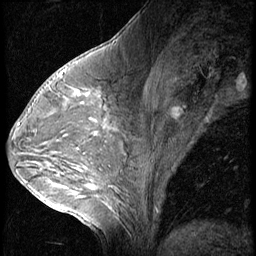
Breast MRI (dynamic contrast-enhanced), one sagittal slice. Position 31 of 56 along the scan axis. 3 images stored at this slice position (order not interpretable as contrast timing). 1.5 T. TE 4.2 ms, TR 9 ms. 256 × 256 image matrix. Patient: female, 54 years. From the clinical record (not read from this slice): setting: breast cancer imaged before/during neoadjuvant chemotherapy; receptor status: triple-negative.
Structures marked on this image (semi-automatically segmented with operator editing):
- analysis volume of interest (the breast-tissue region the enhancement analysis was run in; not a lesion): box from (x=62, y=80) to (x=115, y=128) px
- tumour enhancement mask (voxels above the 140 % enhancement threshold inside the analysis volume of interest): (x=75, y=90)–(x=87, y=96)